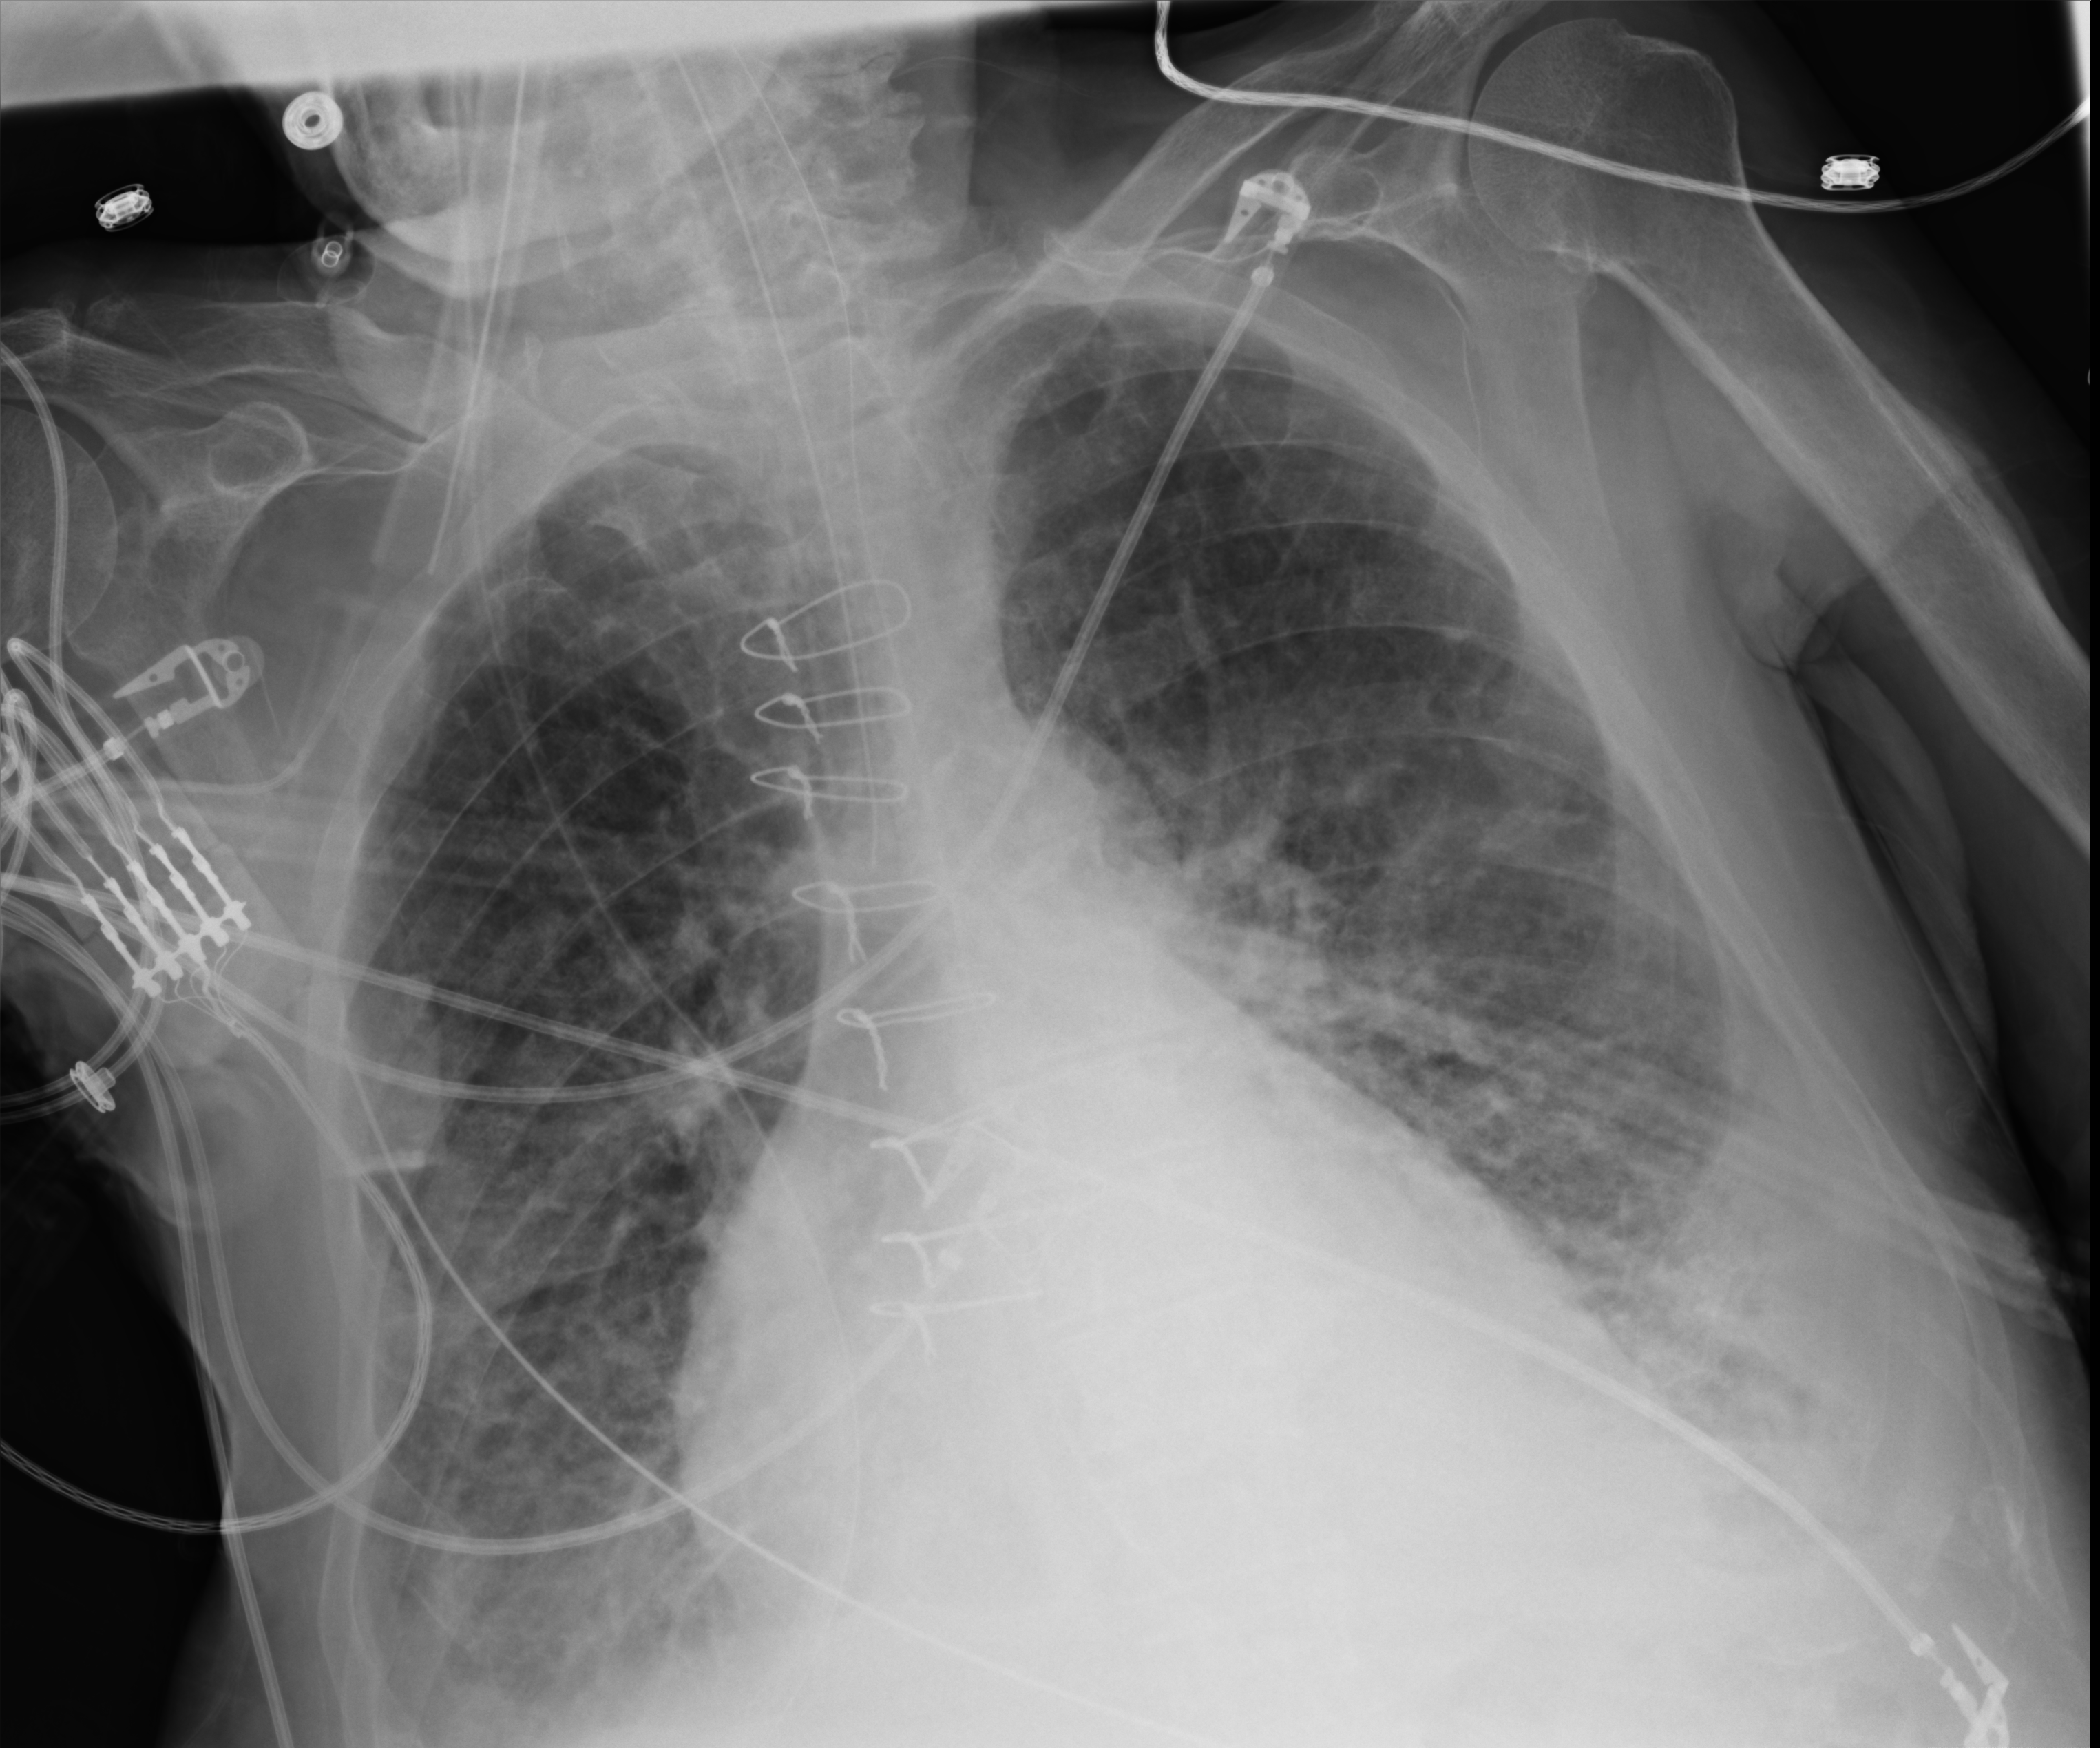
Bedside chest radiograph (computed radiography); anteroposterior (AP) projection. Patient hospitalised with COVID-19; male, aged 75–90 years.
From the hospital-stay record, not from the radiograph (when in the stay this image was taken is not recorded): mechanically ventilated during this hospital stay: yes; admitted to intensive care during this hospital stay: yes.